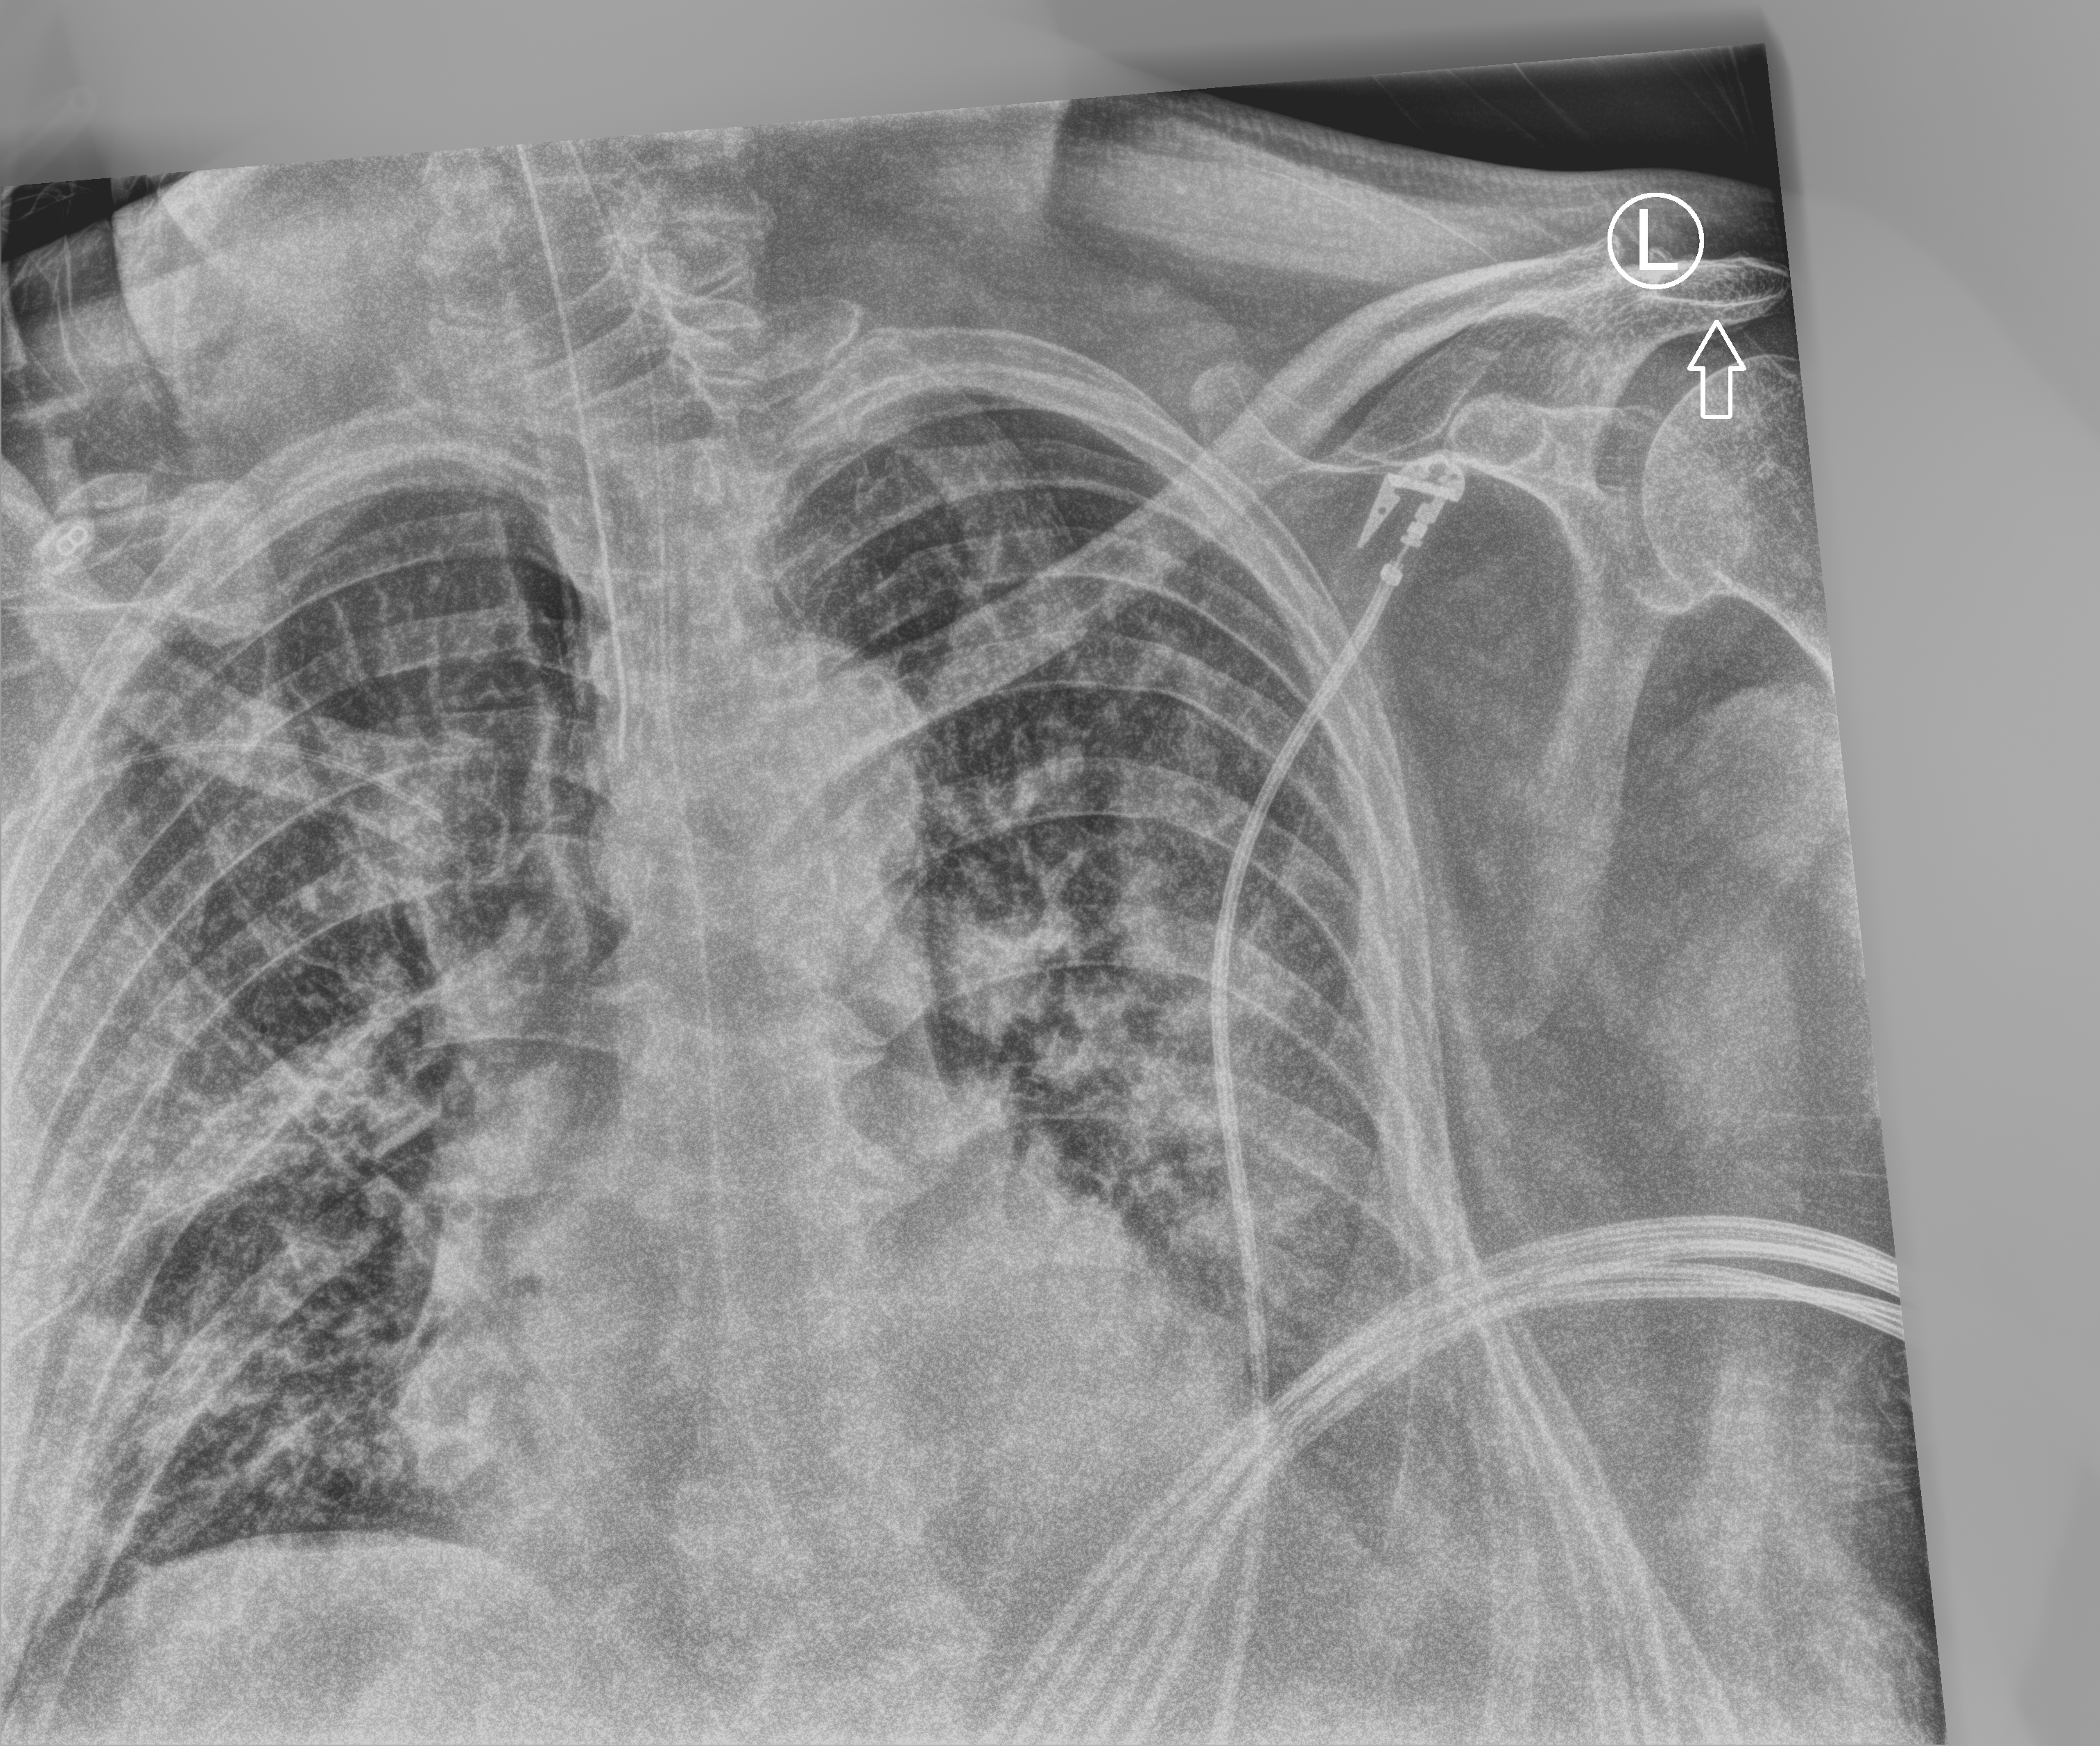
Bedside chest radiograph (computed radiography), anteroposterior (AP) projection. Patient hospitalised with COVID-19; male, aged 60–74 years.
From the hospital-stay record, not from the radiograph (when in the stay this image was taken is not recorded): smoking status (admission record): former; hypertension (admission record): yes.